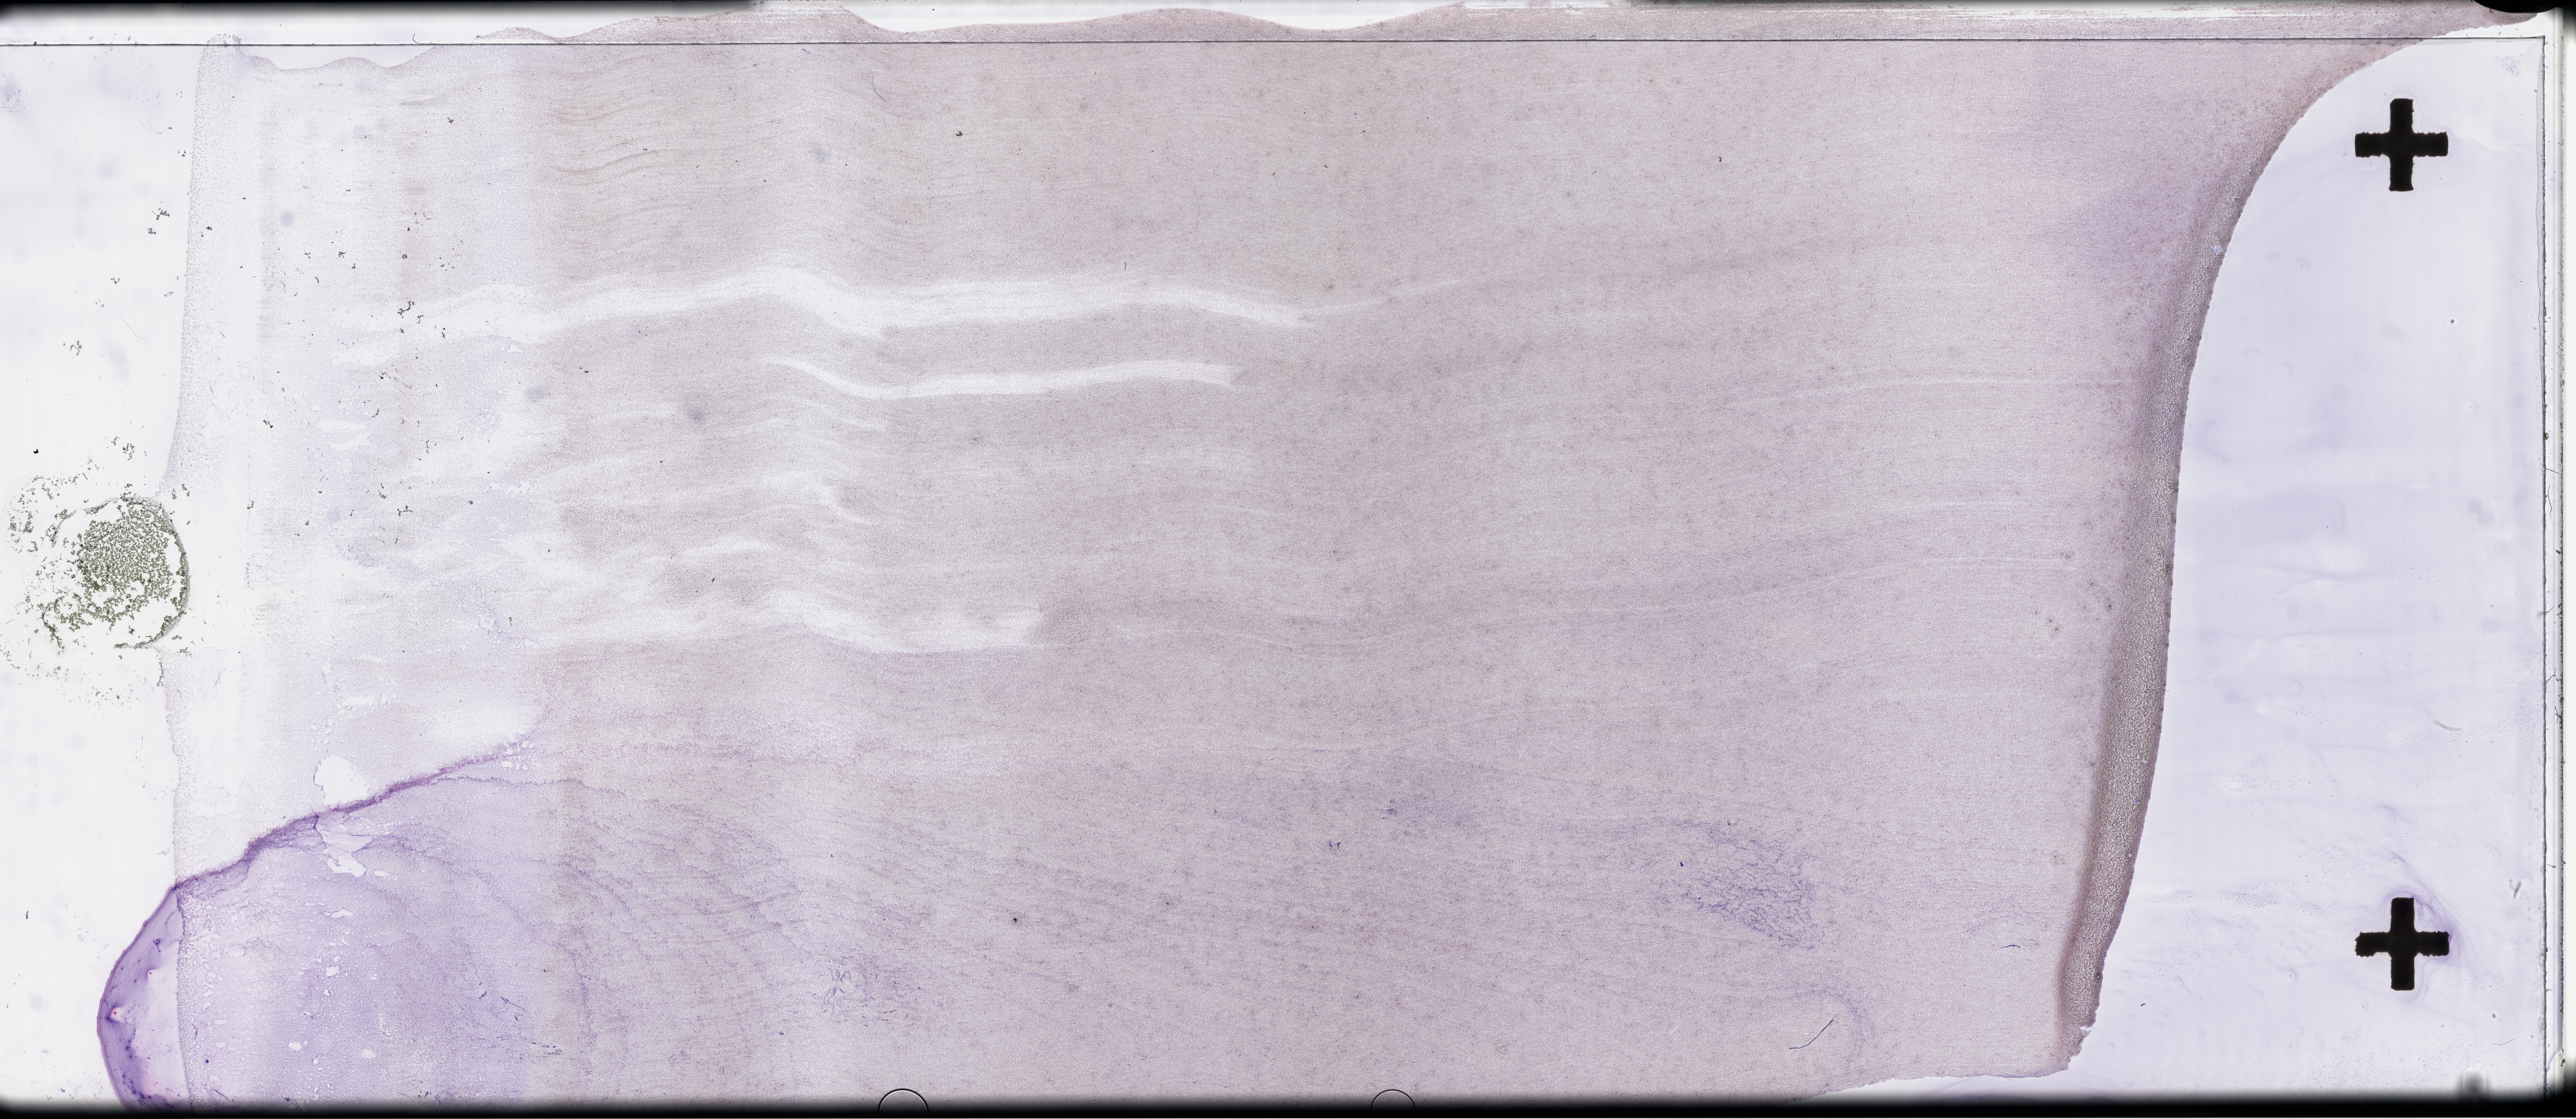
Wright-Giemsa-stained whole blood smear, whole-slide image, a low-resolution overview of the entire scanned area, about 56.3 x 24.5 mm, EDTA-anticoagulated smear, collected on treatment. Female patient.
From a patient with: Plasma Cell Myeloma.